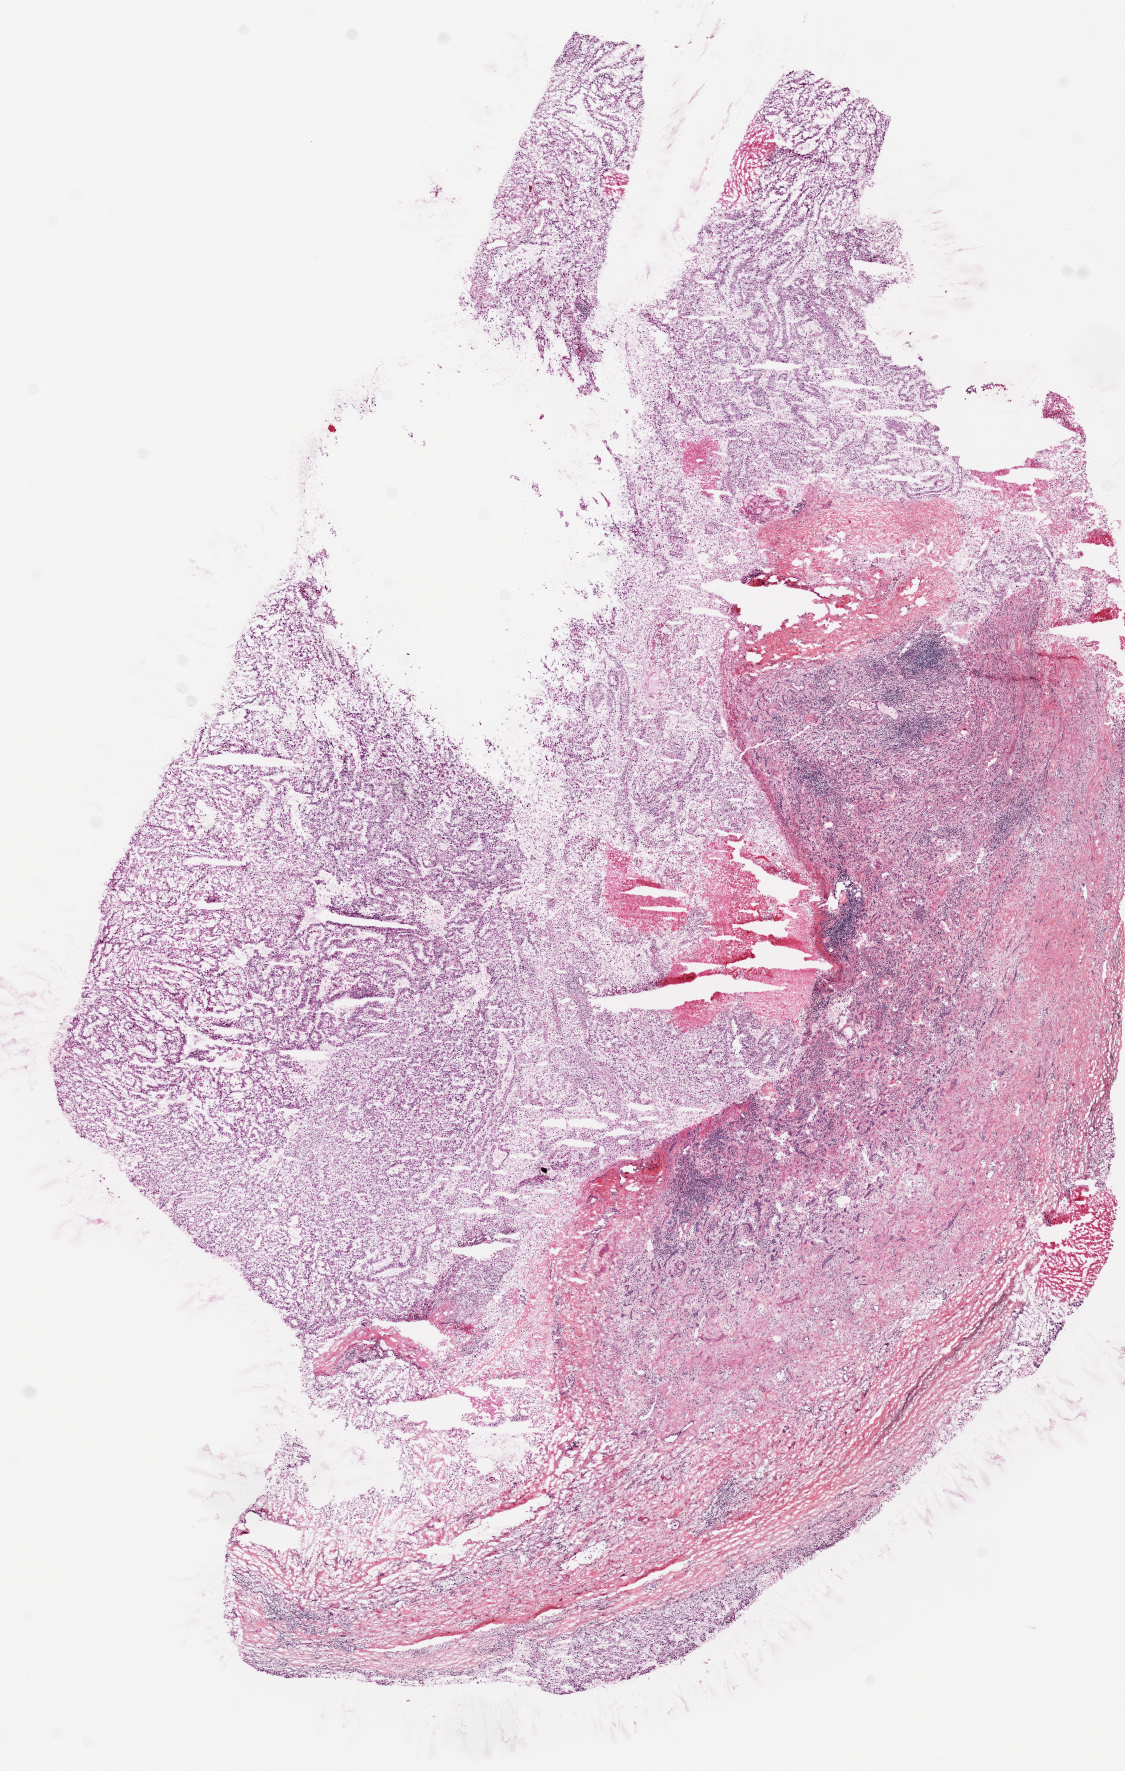
Whole-slide histology image, H&E-stained — low-resolution overview of the scanned area, about 9.0 x 14.2 mm (from a 20x scan), frozen section from the top of the tissue portion, kidney, primary tumour sample. Female, age 64 years at initial diagnosis. Histologic grade: G2 (moderately differentiated). Slide review estimates, as recorded: tumour cells 50%, tumour nuclei 70%, normal cells 0%, stromal cells 45%, necrosis 5%. Infiltration values recorded for this section: lymphocyte infiltration 5%, monocyte infiltration 2%, neutrophil infiltration 1%.
- lymph nodes positive (case pathology): 0 of 7 examined
- histologic diagnosis: Clear cell adenocarcinoma, NOS
- TNM: T1 N0 M0
- AJCC pathologic stage: I